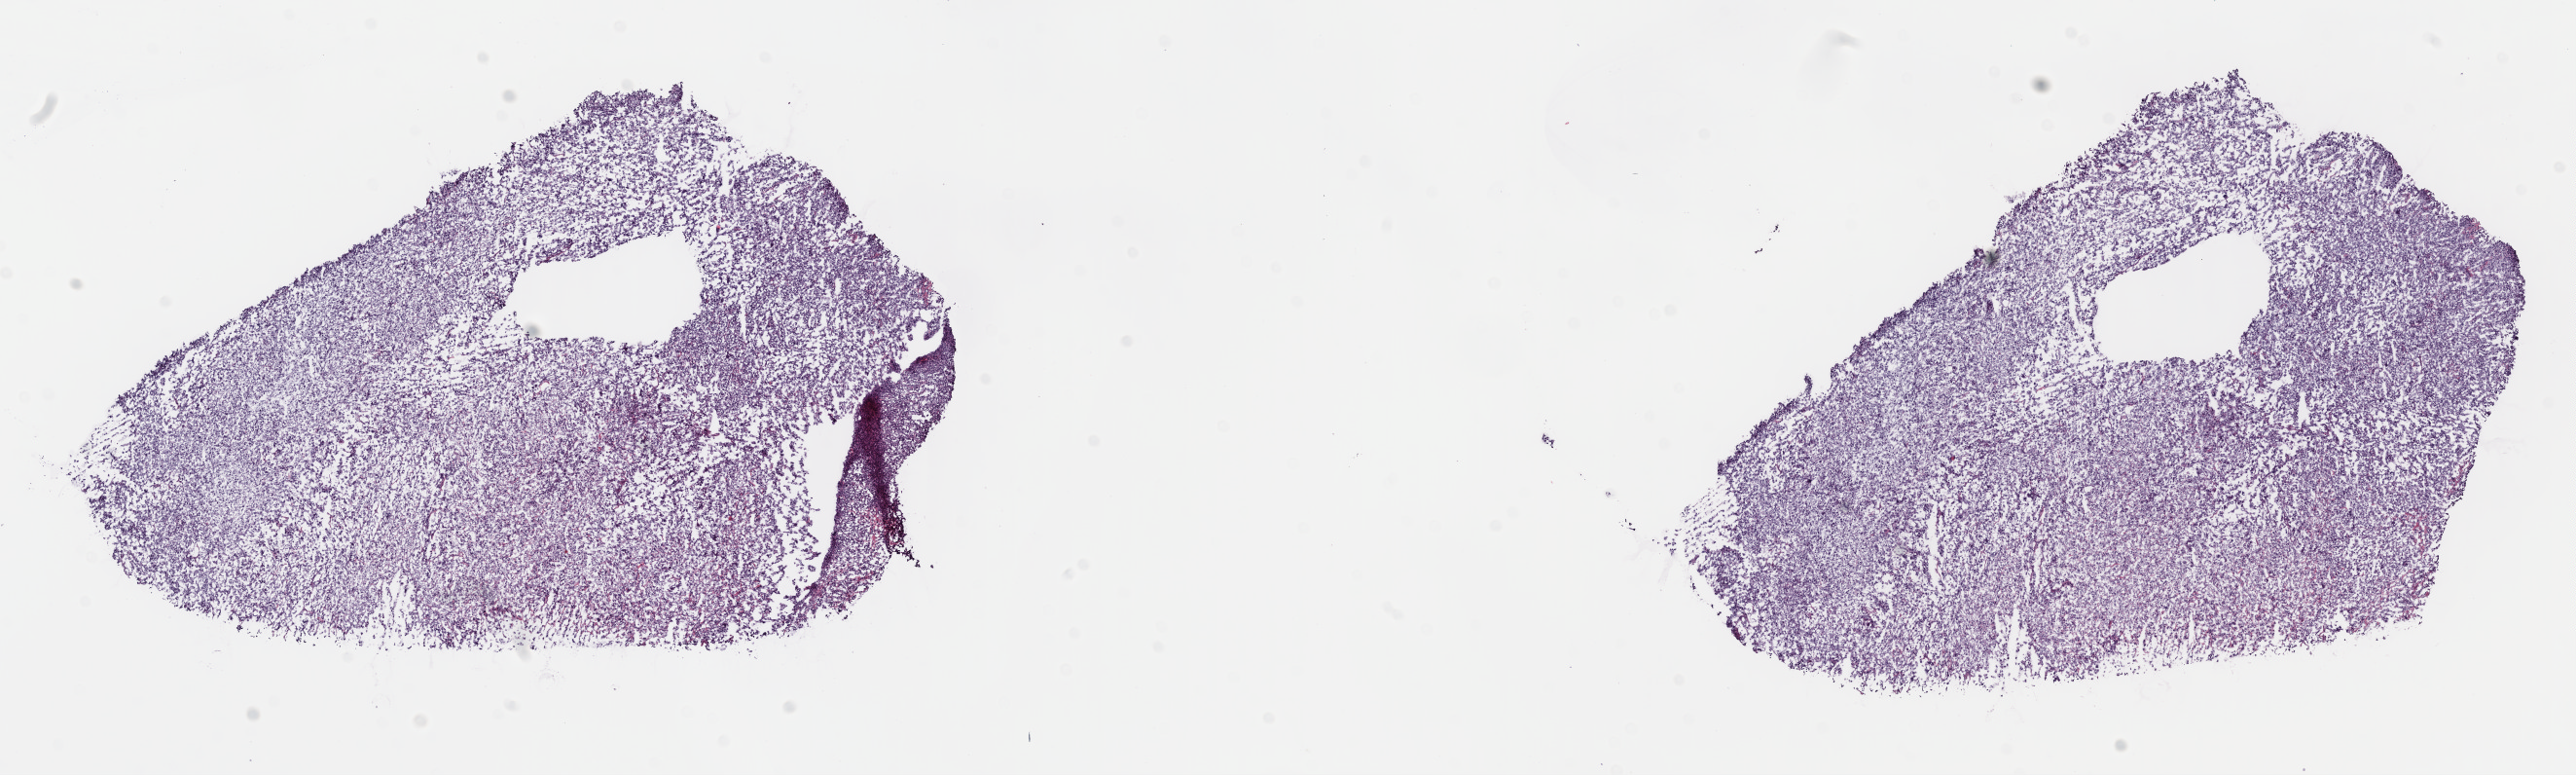
Whole-slide histology image, Hematoxylin and eosin (H&E) stained — a low-resolution overview of the entire scanned area, about 20.8 x 6.3 mm (slide scanned at 40x), frozen section, sample: primary tumour, uterus. Female patient; age at initial diagnosis 69 years.
Pathologic diagnosis: Leiomyosarcoma, NOS.